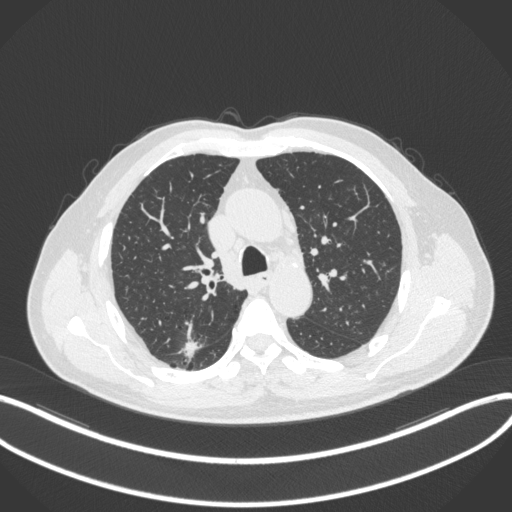
Chest CT, one axial slice; position 256 of 366 along the scan axis; reconstruction kernel B31f; lung window (W 1500 / L -600 HU); 1 mm slice thickness; 512 × 512 image matrix, field of view 400 × 400 mm. Patient: male, 69 years. Case-level facts recorded for this patient, not image findings: clinical TNM (as recorded): T1b N0 M0.
Outlined on this slice (bounding box drawn by a radiologist):
- lung tumour (recorded histology: adenocarcinoma): bounding box (x1, y1, x2, y2) in pixels: (176, 334, 203, 365)